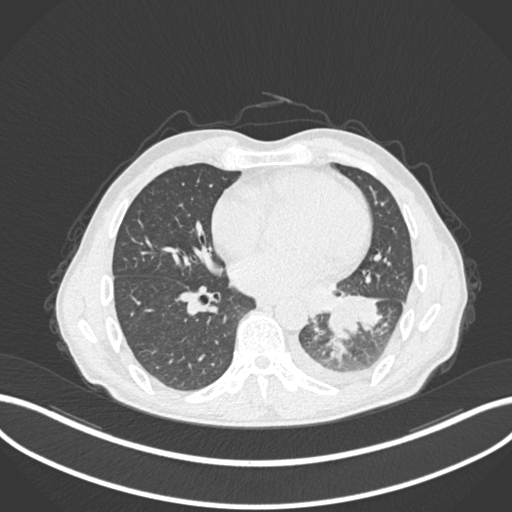
Chest CT, one axial slice; position 102 of 222 along the scan axis; 120 kVp; lung window (W 1500 / L -600 HU); 1 mm slice thickness; 512 × 512 image matrix, field of view 400 × 400 mm. Male patient, age 47 years. Case-level facts recorded for this patient, not image findings: clinical TNM (as recorded): T3 N1 M1c.
Outlined on this slice (rectangle marked by the reading radiologist):
- lung tumour (recorded histology: small cell carcinoma): bounding box [x1, y1, x2, y2] px = [325, 297, 359, 339]